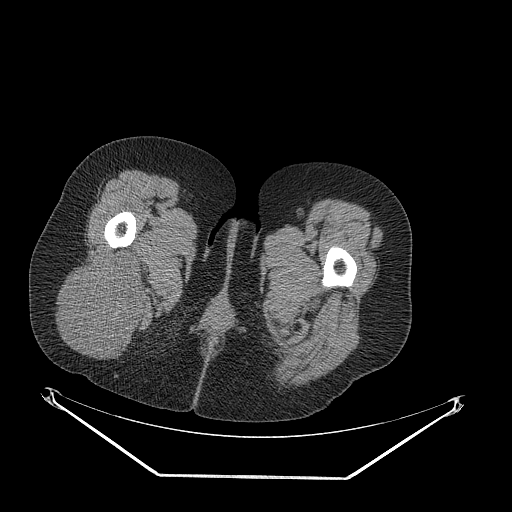
CT of an extremity soft-tissue mass (from a PET/CT study), one axial slice. Position 48 of 257 along the scan axis. Soft-tissue window (W 400 / L 40 HU). 3.75 mm slice thickness. 512 × 512 image matrix, field of view 500 × 500 mm. Female patient. From the clinical record (not read from this slice): histological type: synovial sarcoma; grade: intermediate; site of the primary tumour: right buttock.
Annotated regions visible in this slice (expert contour drawn on MRI and transferred to this co-registered scan by the dataset authors):
- gross tumour volume including surrounding oedema: bounding box (x1, y1, x2, y2) in pixels: (64, 251, 147, 350)
- gross tumour volume (mass): (64, 251, 147, 350)